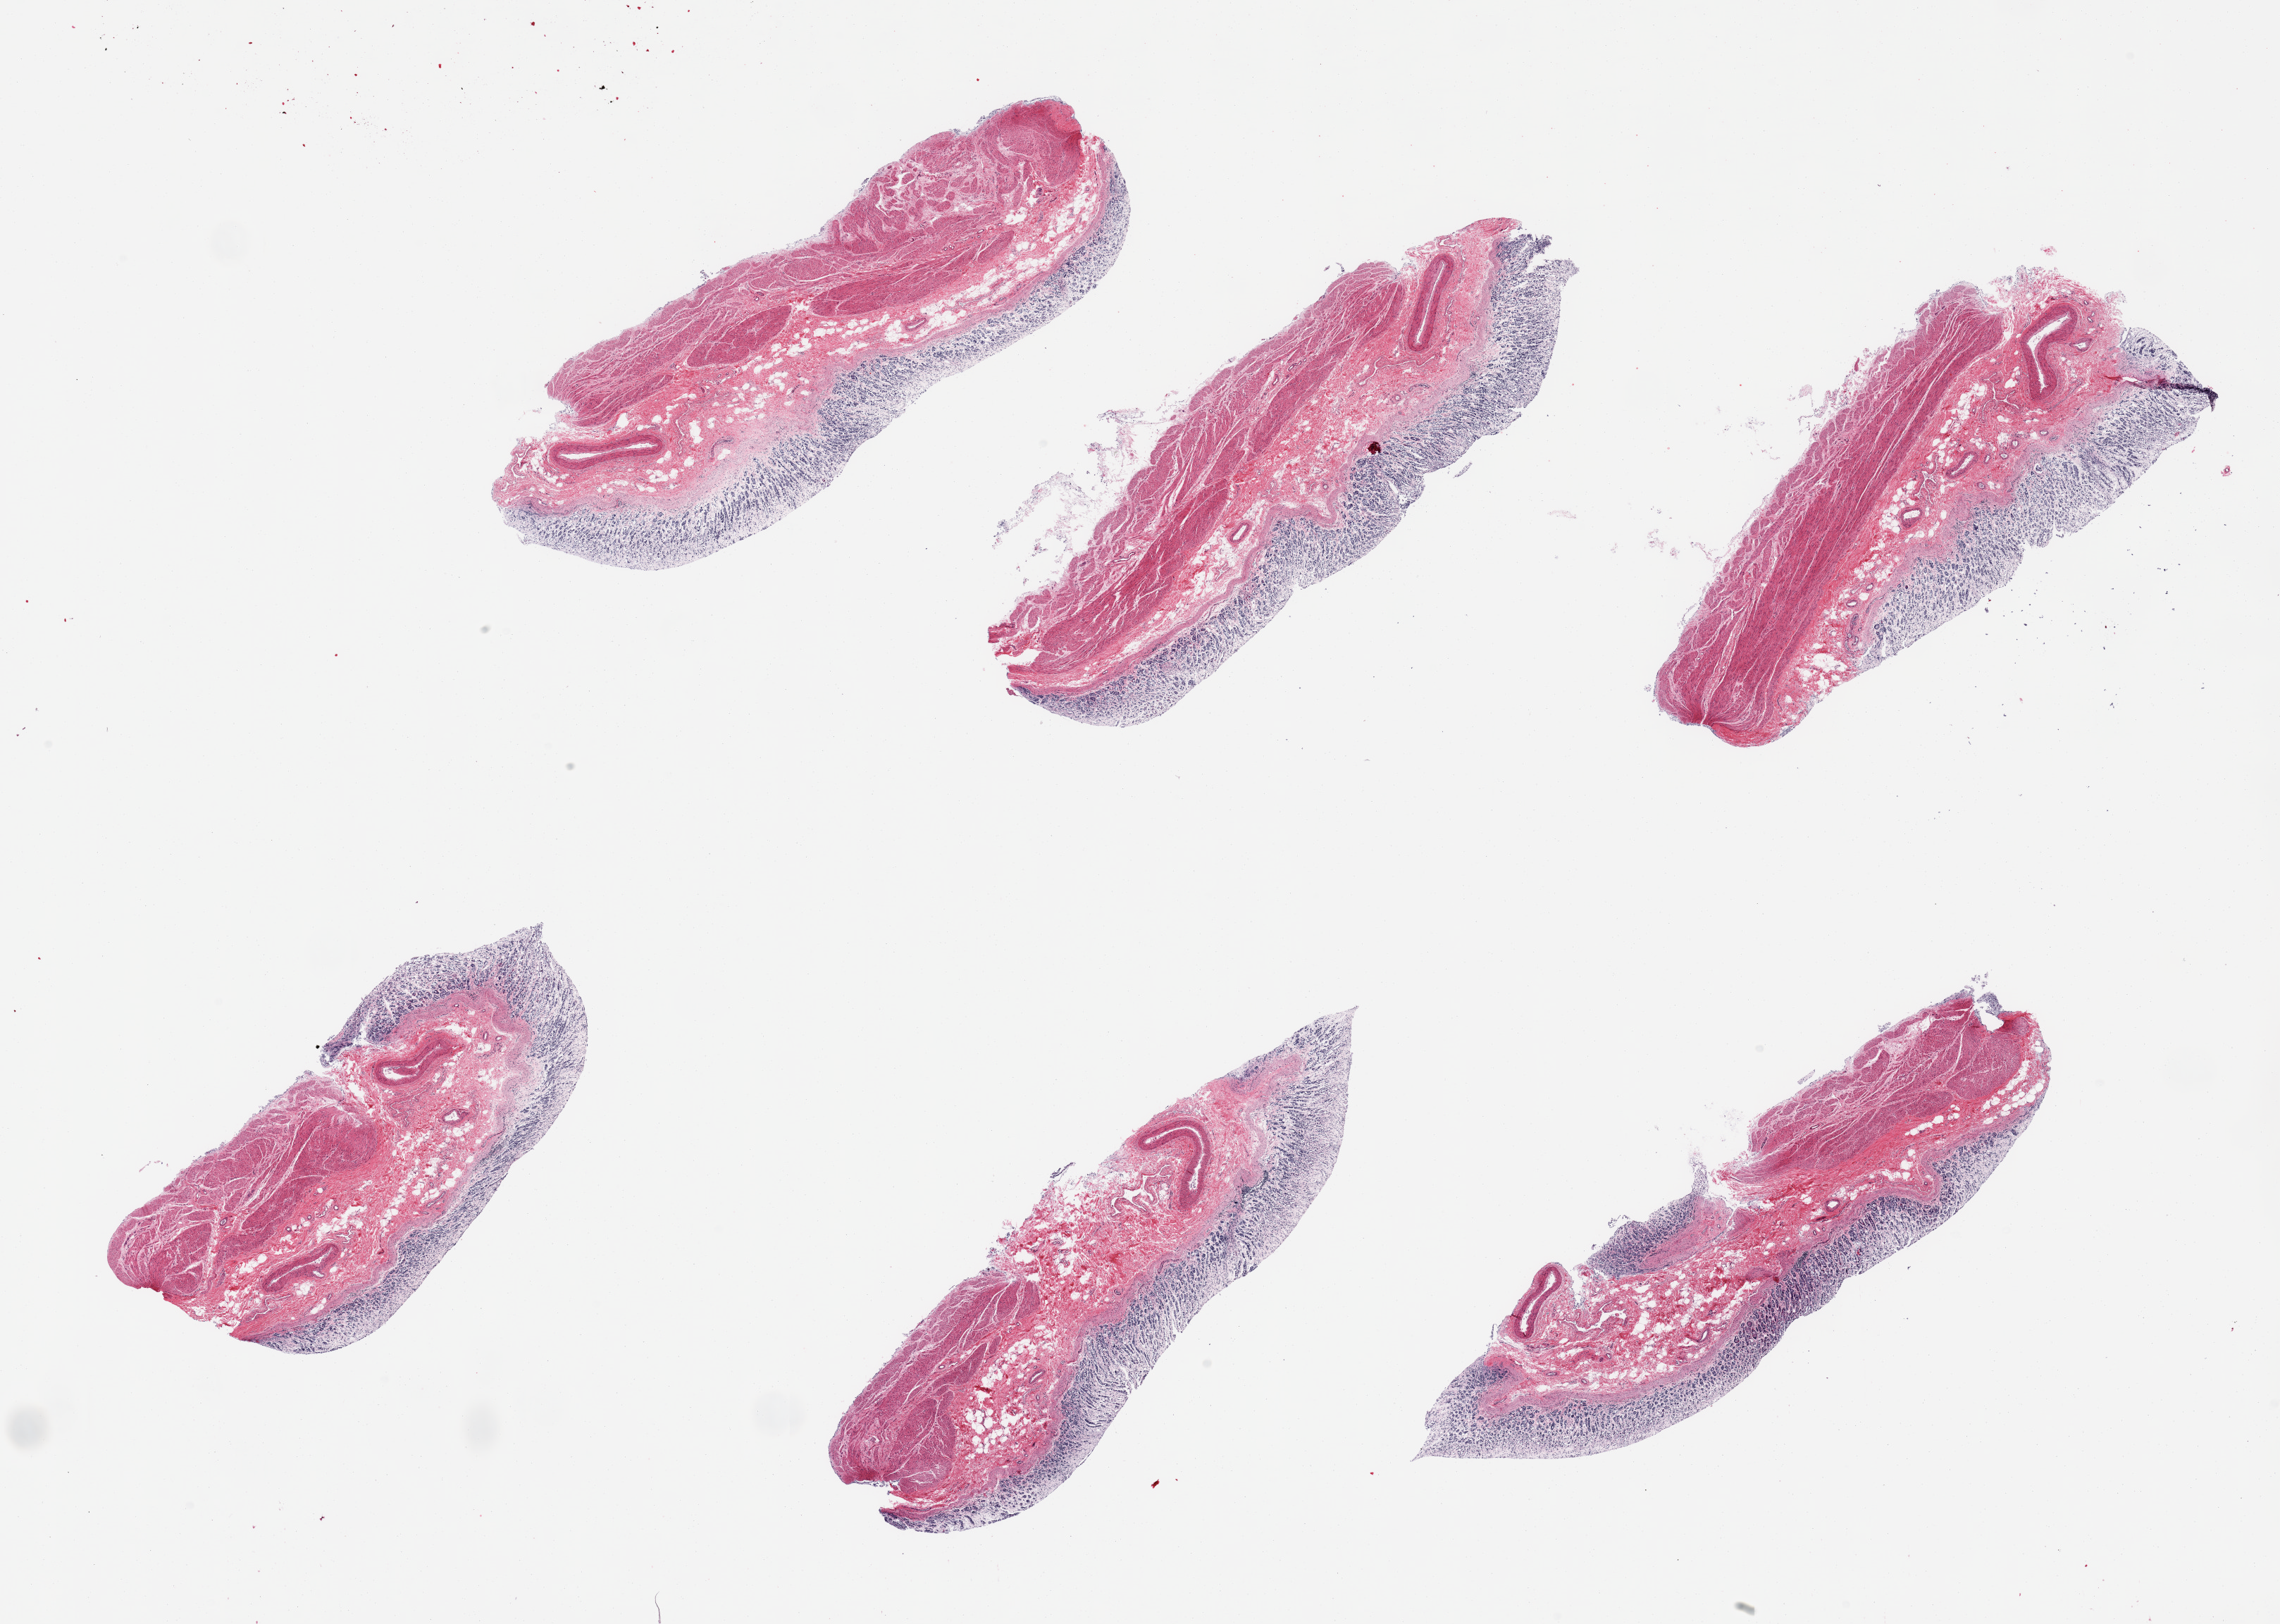
Digitized H&E-stained section, low-resolution overview of the scanned area, about 25.6 x 18.2 mm, PAXgene-fixed paraffin-embedded (PFPE) section, section of stomach (target tissue), tissue donor sample. Male donor.
Reviewer comment on this tissue sample: 6 pieces; mucosa=3;muscle=2.